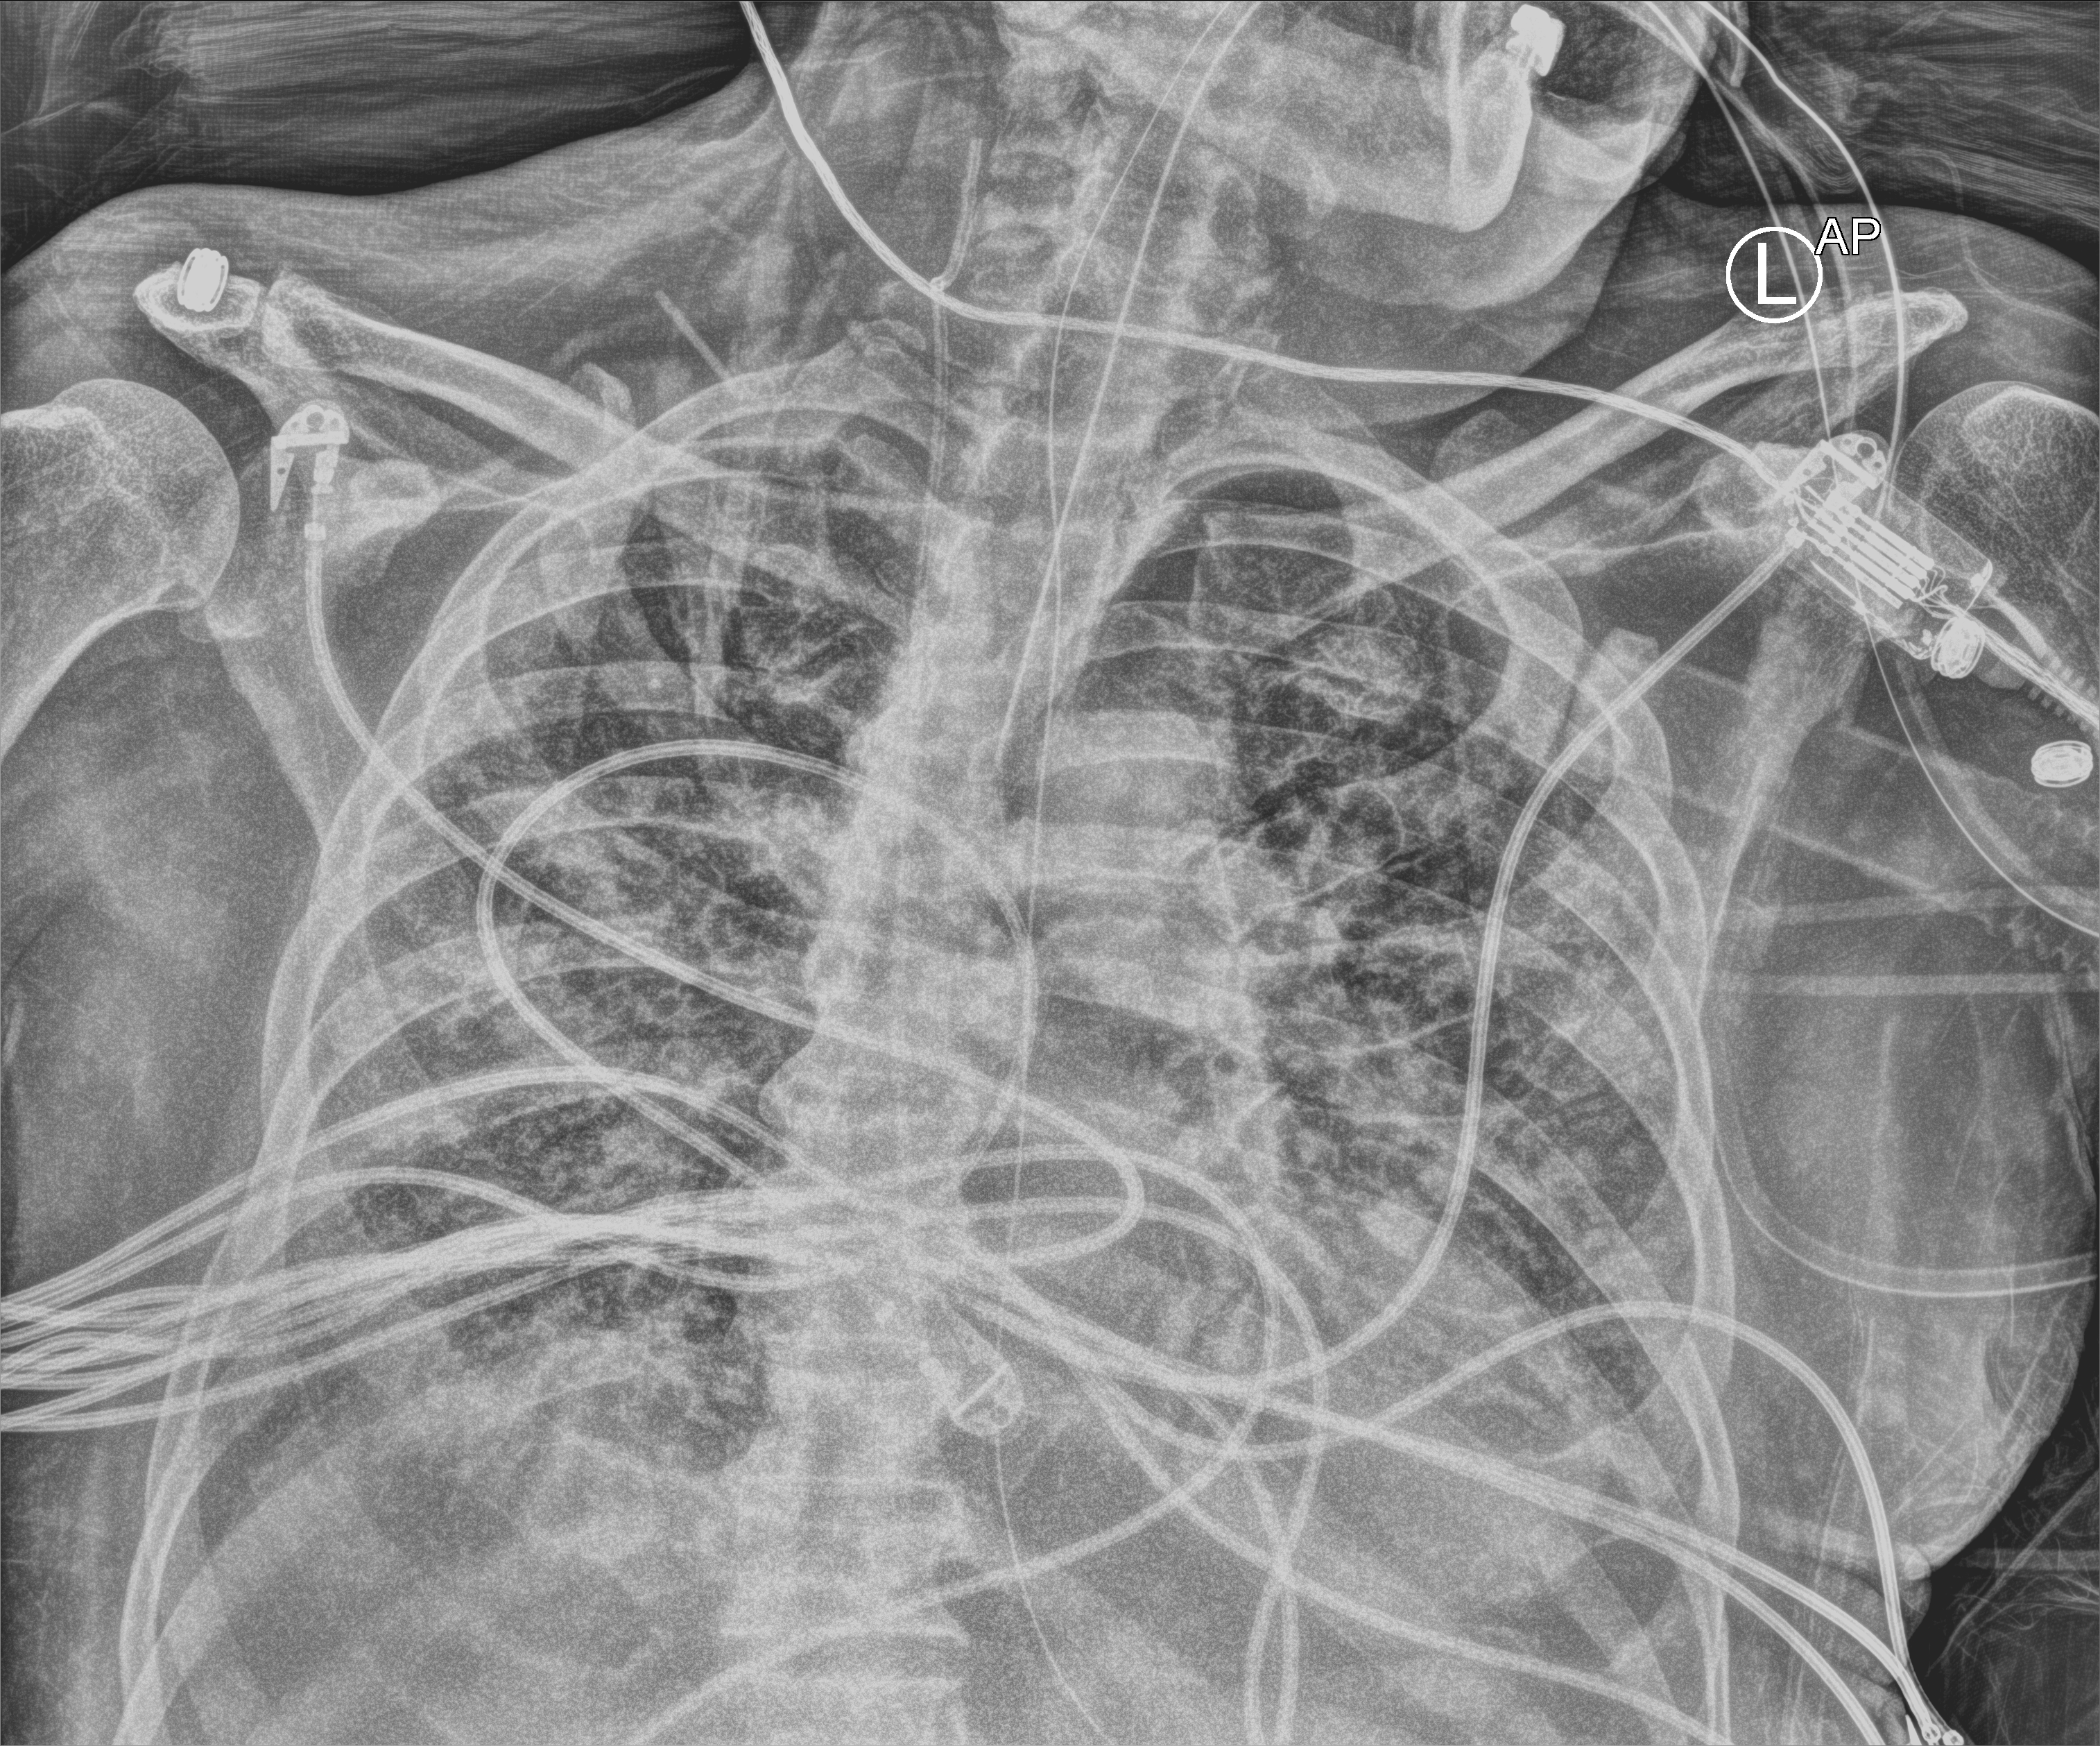
Bedside chest radiograph (computed radiography); anteroposterior (AP) projection. Male patient hospitalised with COVID-19, age 75–90 years.
Admission-level facts for this patient (not findings on this image; timing relative to this image not recorded):
- length of hospital stay: 33 days